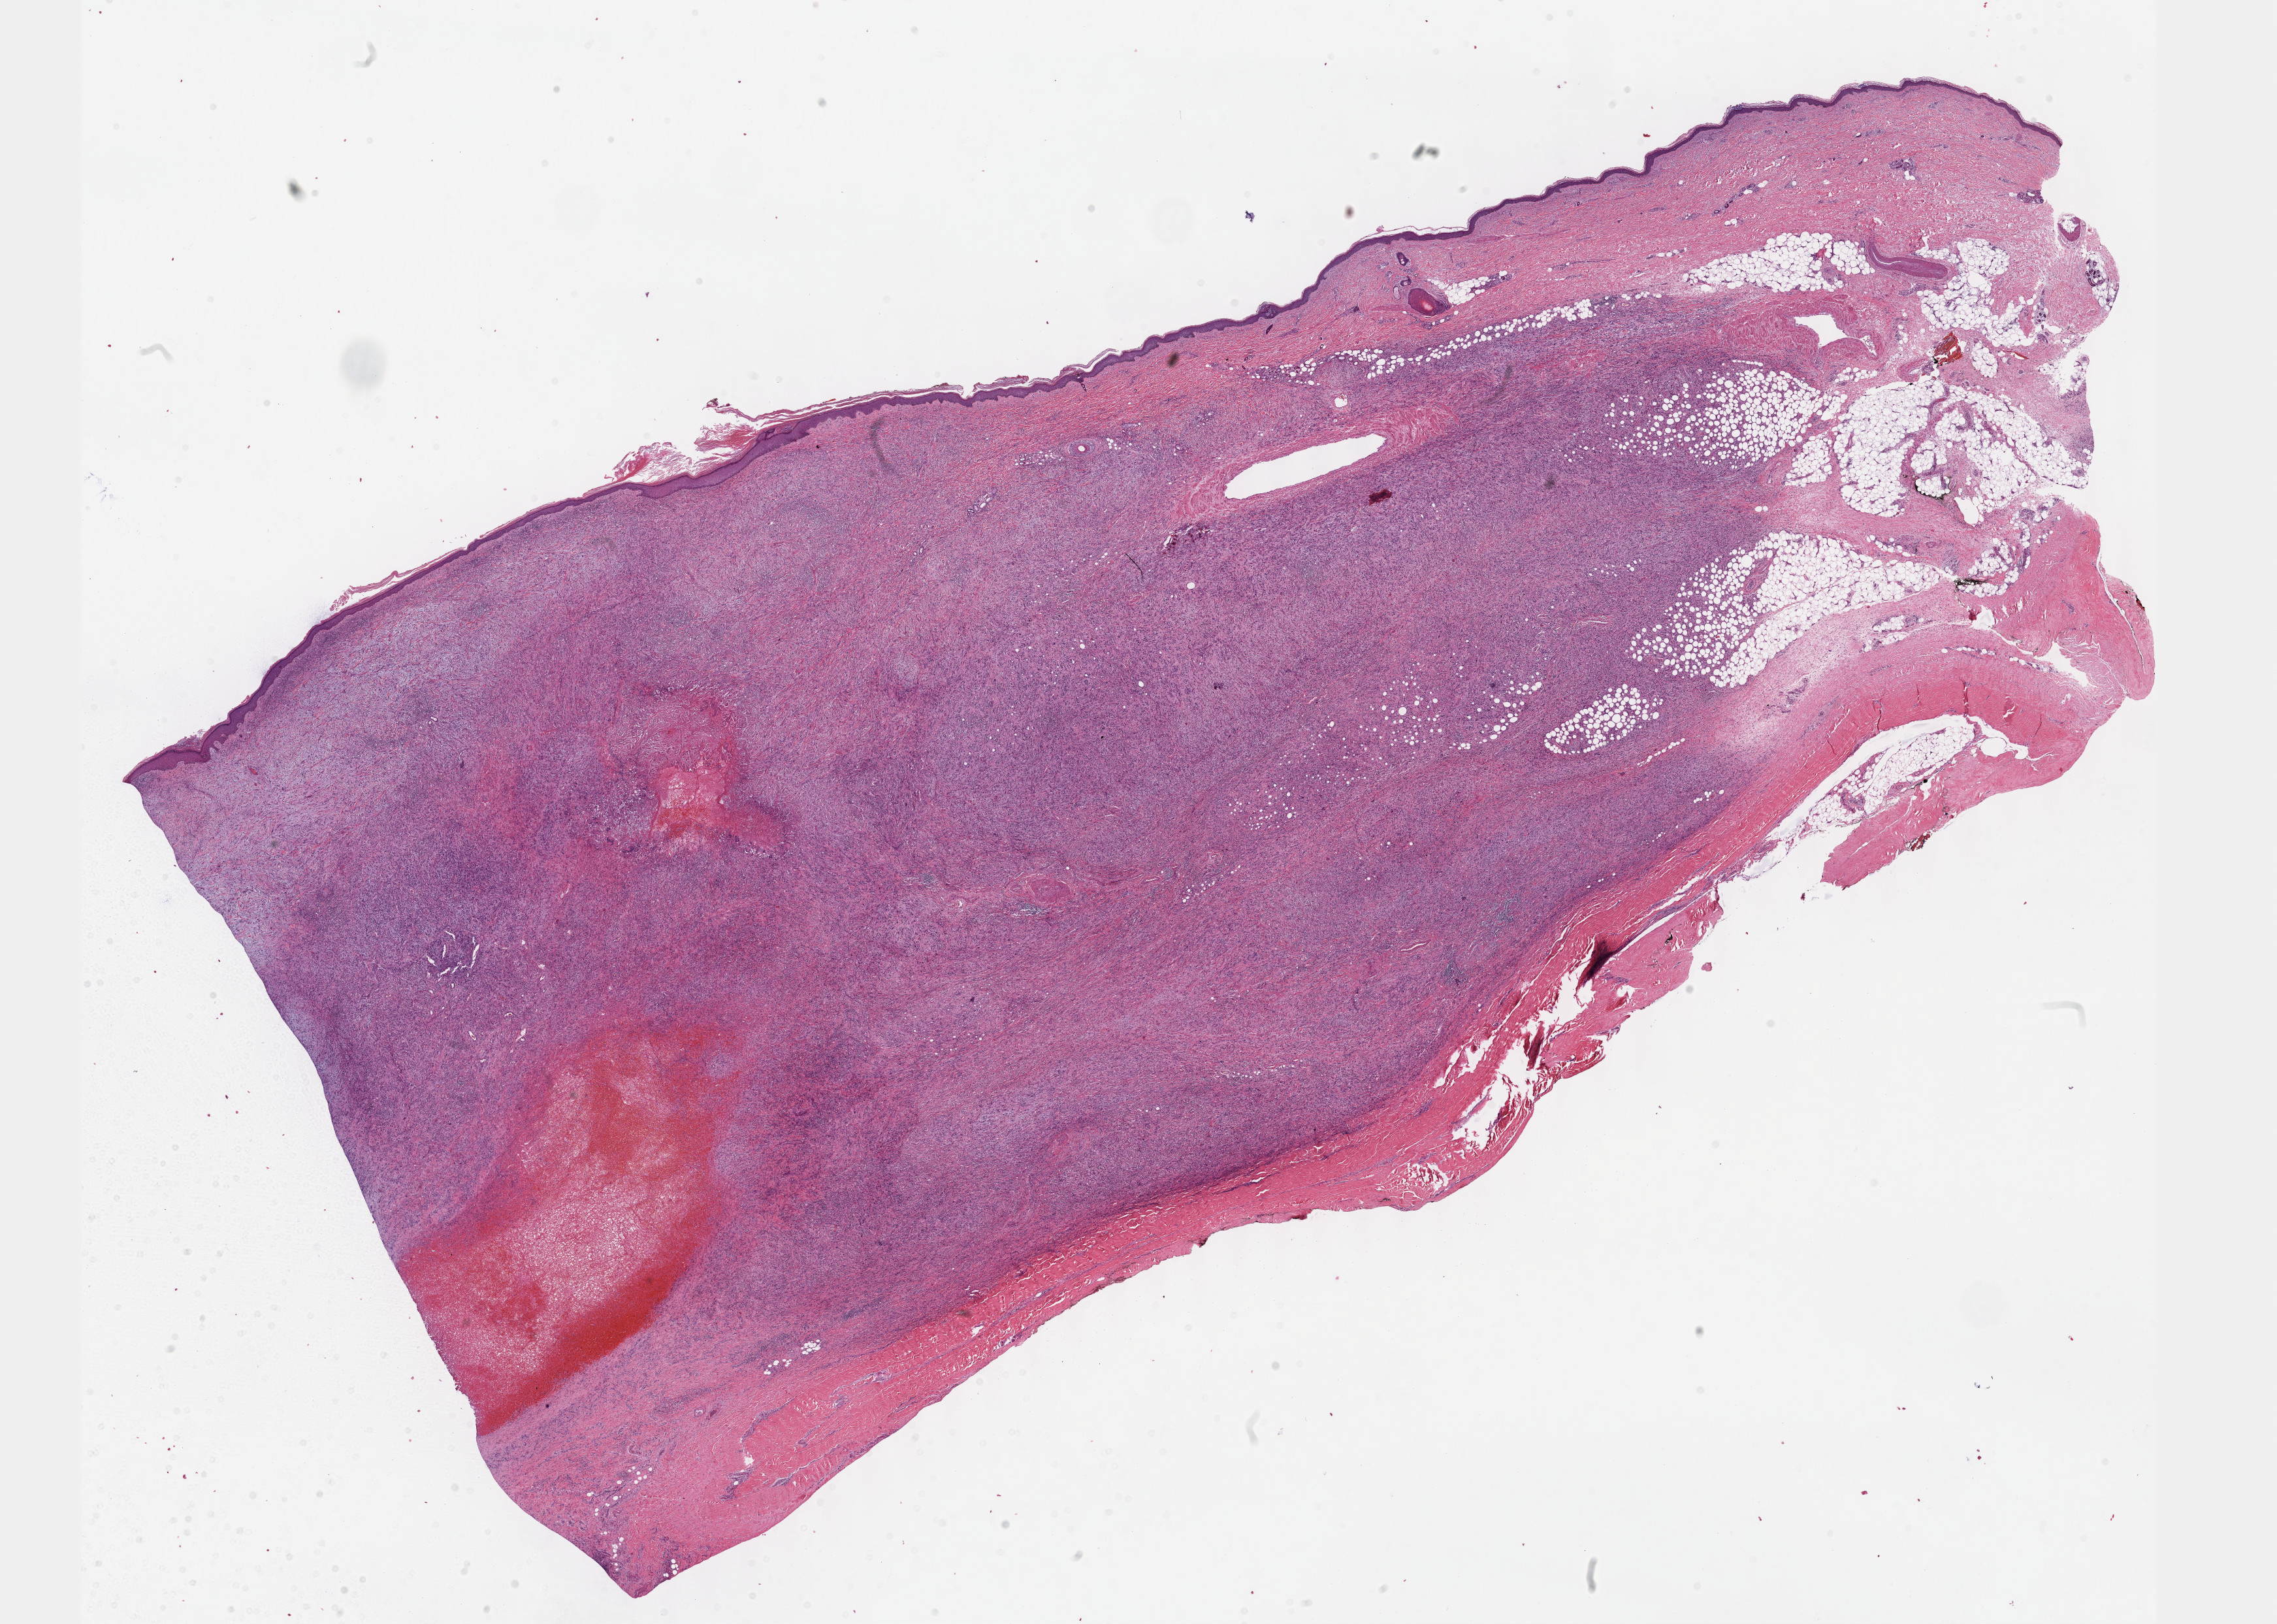
H&E-stained whole-slide image — whole scanned area (about 28.2 x 20.1 mm) shown as a low-resolution overview, formalin-fixed paraffin-embedded (FFPE) diagnostic section, primary tumour sample from the connective, subcutaneous and other soft tissues. Patient: female, age at initial diagnosis 49 years.
Histologic diagnosis: Undifferentiated sarcoma (connective, subcutaneous and other soft tissues of lower limb and hip).